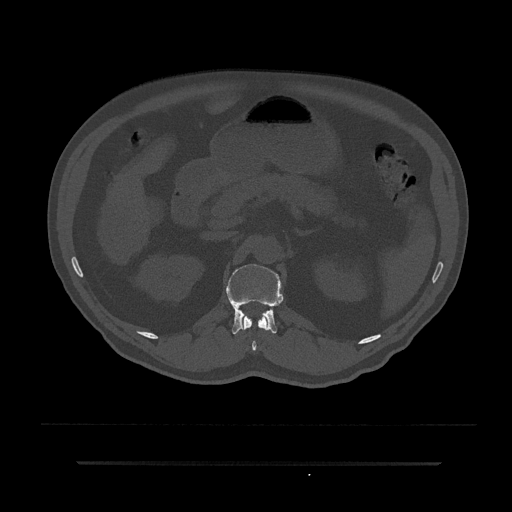
CT including the spine, one axial slice; slice 171 of 797 in the series (ordered by position); reconstruction kernel Br40s/3; 120 kVp; bone window (W 1800 / L 400 HU); 512 × 512 image matrix, field of view 464 × 464 mm. Male patient, age 59 years. From the clinical record (not read from this slice): primary cancer: bile ducts.
Outlined on this slice (semi-automatically segmented with operator editing):
- L1 vertebra: box from (x=226, y=264) to (x=283, y=334) px
- T12 vertebra: (x=241, y=315)–(x=268, y=351)